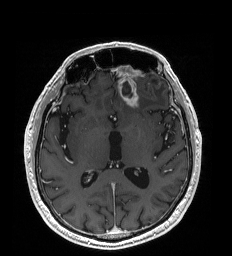
Brain MRI from a brain-tumour surgery series, one axial slice. Slice 103 of 192 in the series (ordered by position). T1-weighted post-contrast. 1 mm slice thickness. 232 × 256 image matrix, field of view 227 × 250 mm. From the clinical record (not read from this slice): histopathology: Glioblastoma; WHO grade: 4; IDH mutation: no.
Outlined on this slice (manually delineated by an expert):
- tumour: box from (x=121, y=85) to (x=138, y=106) px